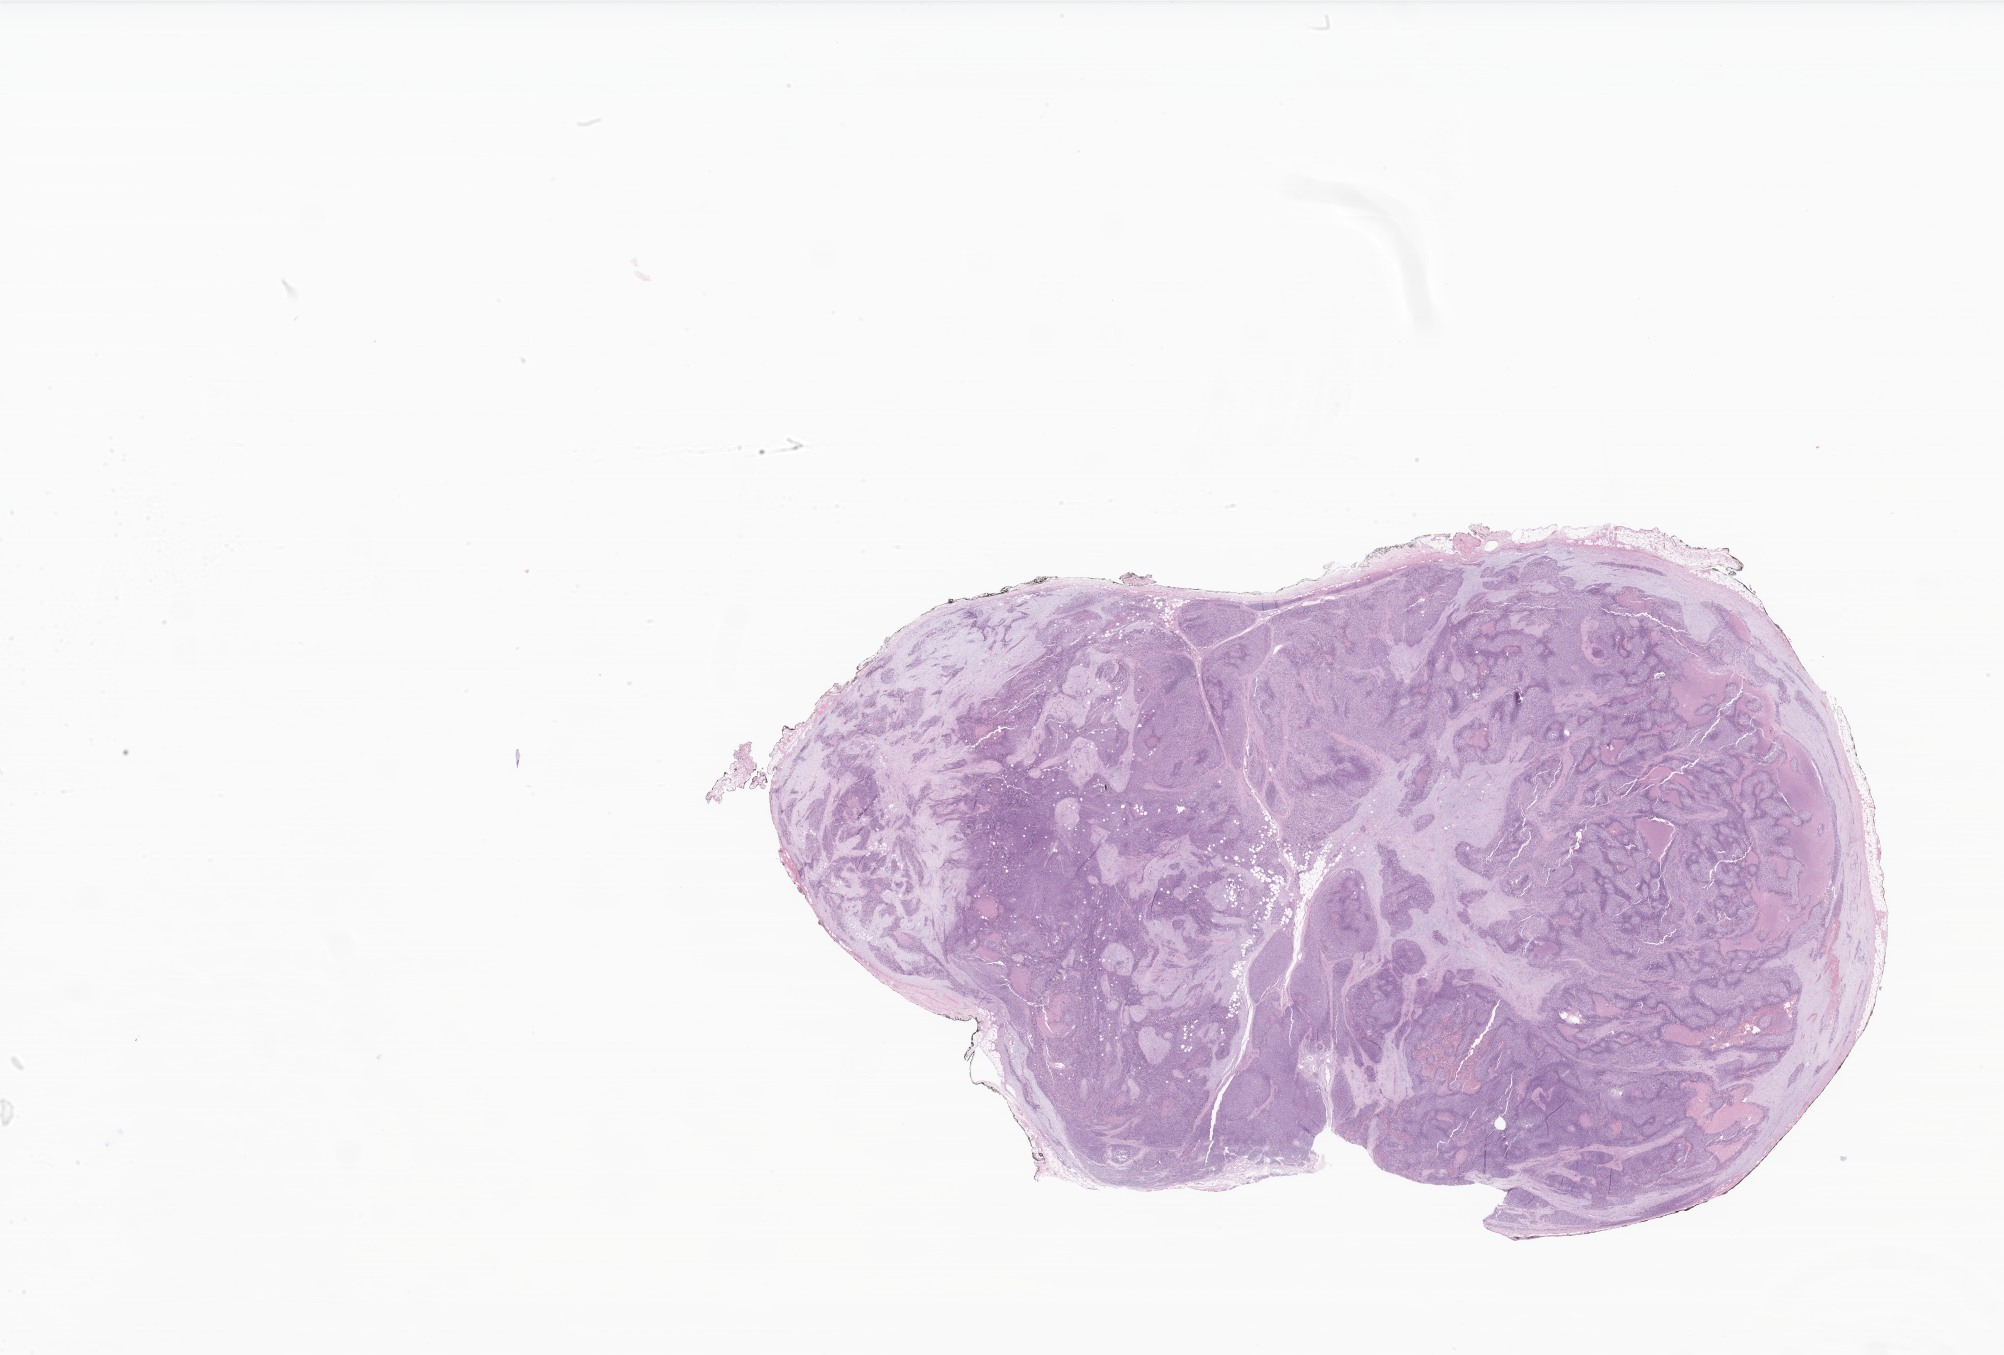
Whole-slide image, H&E stain of tumor tissue from the kidney, a low-resolution overview of the entire scanned area, about 33.8 x 22.9 mm, formalin-fixed paraffin-embedded section. Patient male; age 285 months (23 years 9 months).
Recorded diagnosis: Desmoplastic small round cell tumor.